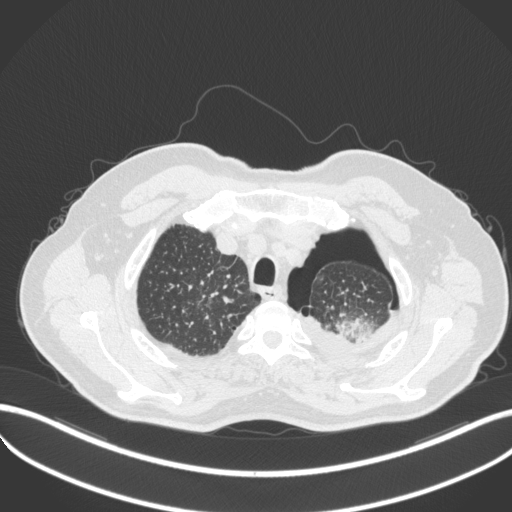
Chest CT, one axial slice; slice 423 of 466 in the series (ordered by position); 120 kVp; lung window (W 1500 / L -600 HU); 1 mm slice thickness; 512 × 512 image matrix, field of view 400 × 400 mm. Male patient, age 76 years. From the clinical record (not read from this slice): clinical TNM (as recorded): T3 N0 M1b.
Outlined on this slice (rectangle marked by the reading radiologist):
- lung tumour (recorded histology: adenocarcinoma): box from (x=335, y=311) to (x=377, y=342) px